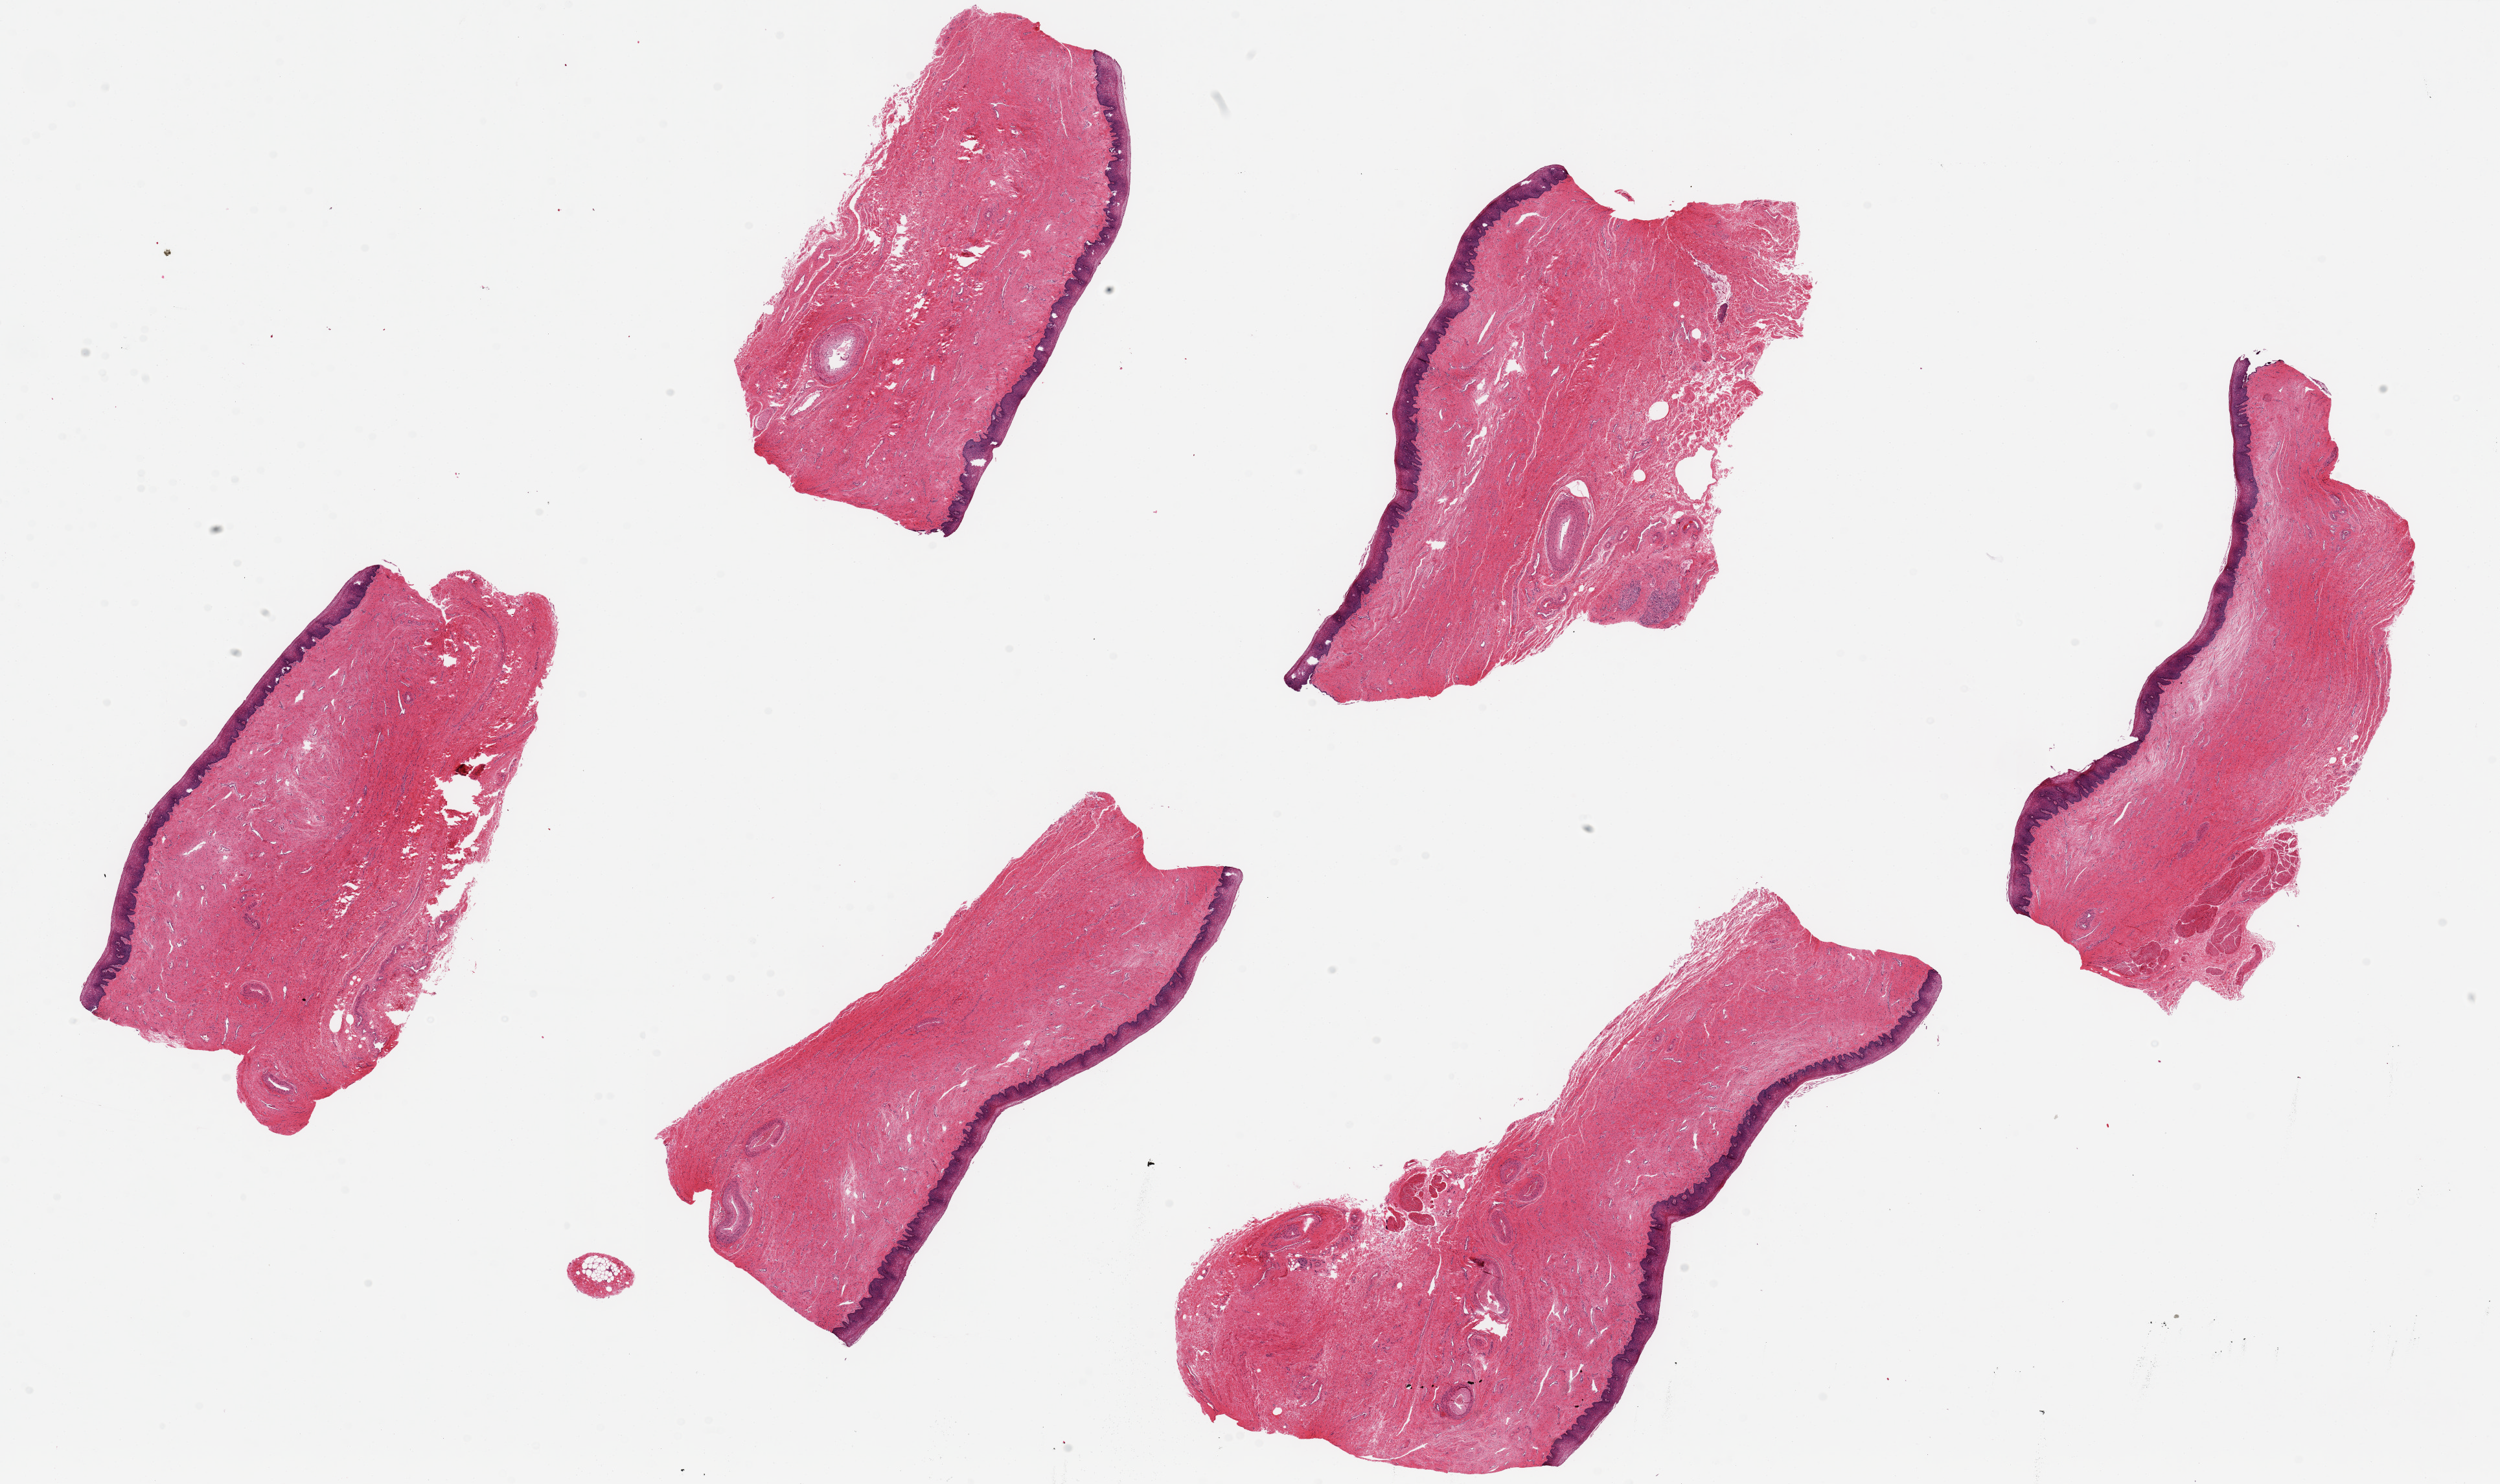
Whole-slide image, hematoxylin and eosin (H&E) stain — shown as a low-resolution overview of the whole scanned area (about 30.5 x 18.1 mm, acquisition: 20x scan); PAXgene-fixed paraffin-embedded (PFPE) section; section of vagina (target tissue); tissue donor sample. Donor: female.
Pathologist's review note for this sample: 6 pieces, 7x2.5mm. Squamous mucosa is ~10% of thickness.